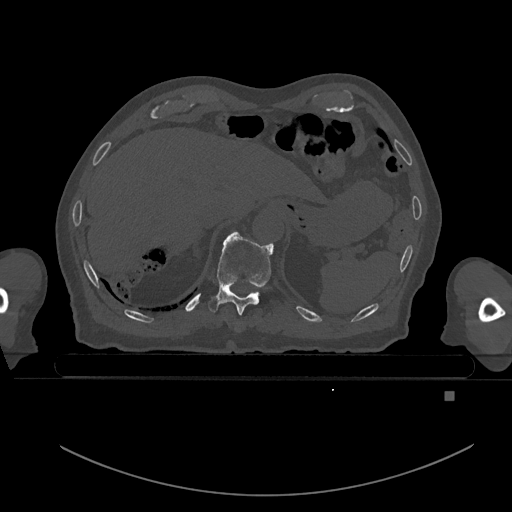
CT including the spine, one axial slice; position 85 of 969 along the scan axis; bone window (W 1800 / L 400 HU); 0.5 mm slice thickness; 512 × 512 image matrix. Male patient, age 82 years. Case-level facts recorded for this patient, not image findings: primary cancer: prostate; vertebrae with lytic lesions (as recorded): T11, T9, T8, T2.
Annotated regions visible in this slice (semi-automatically segmented with operator editing):
- T10 vertebra: bounding box [x1, y1, x2, y2] px = [208, 232, 274, 314]